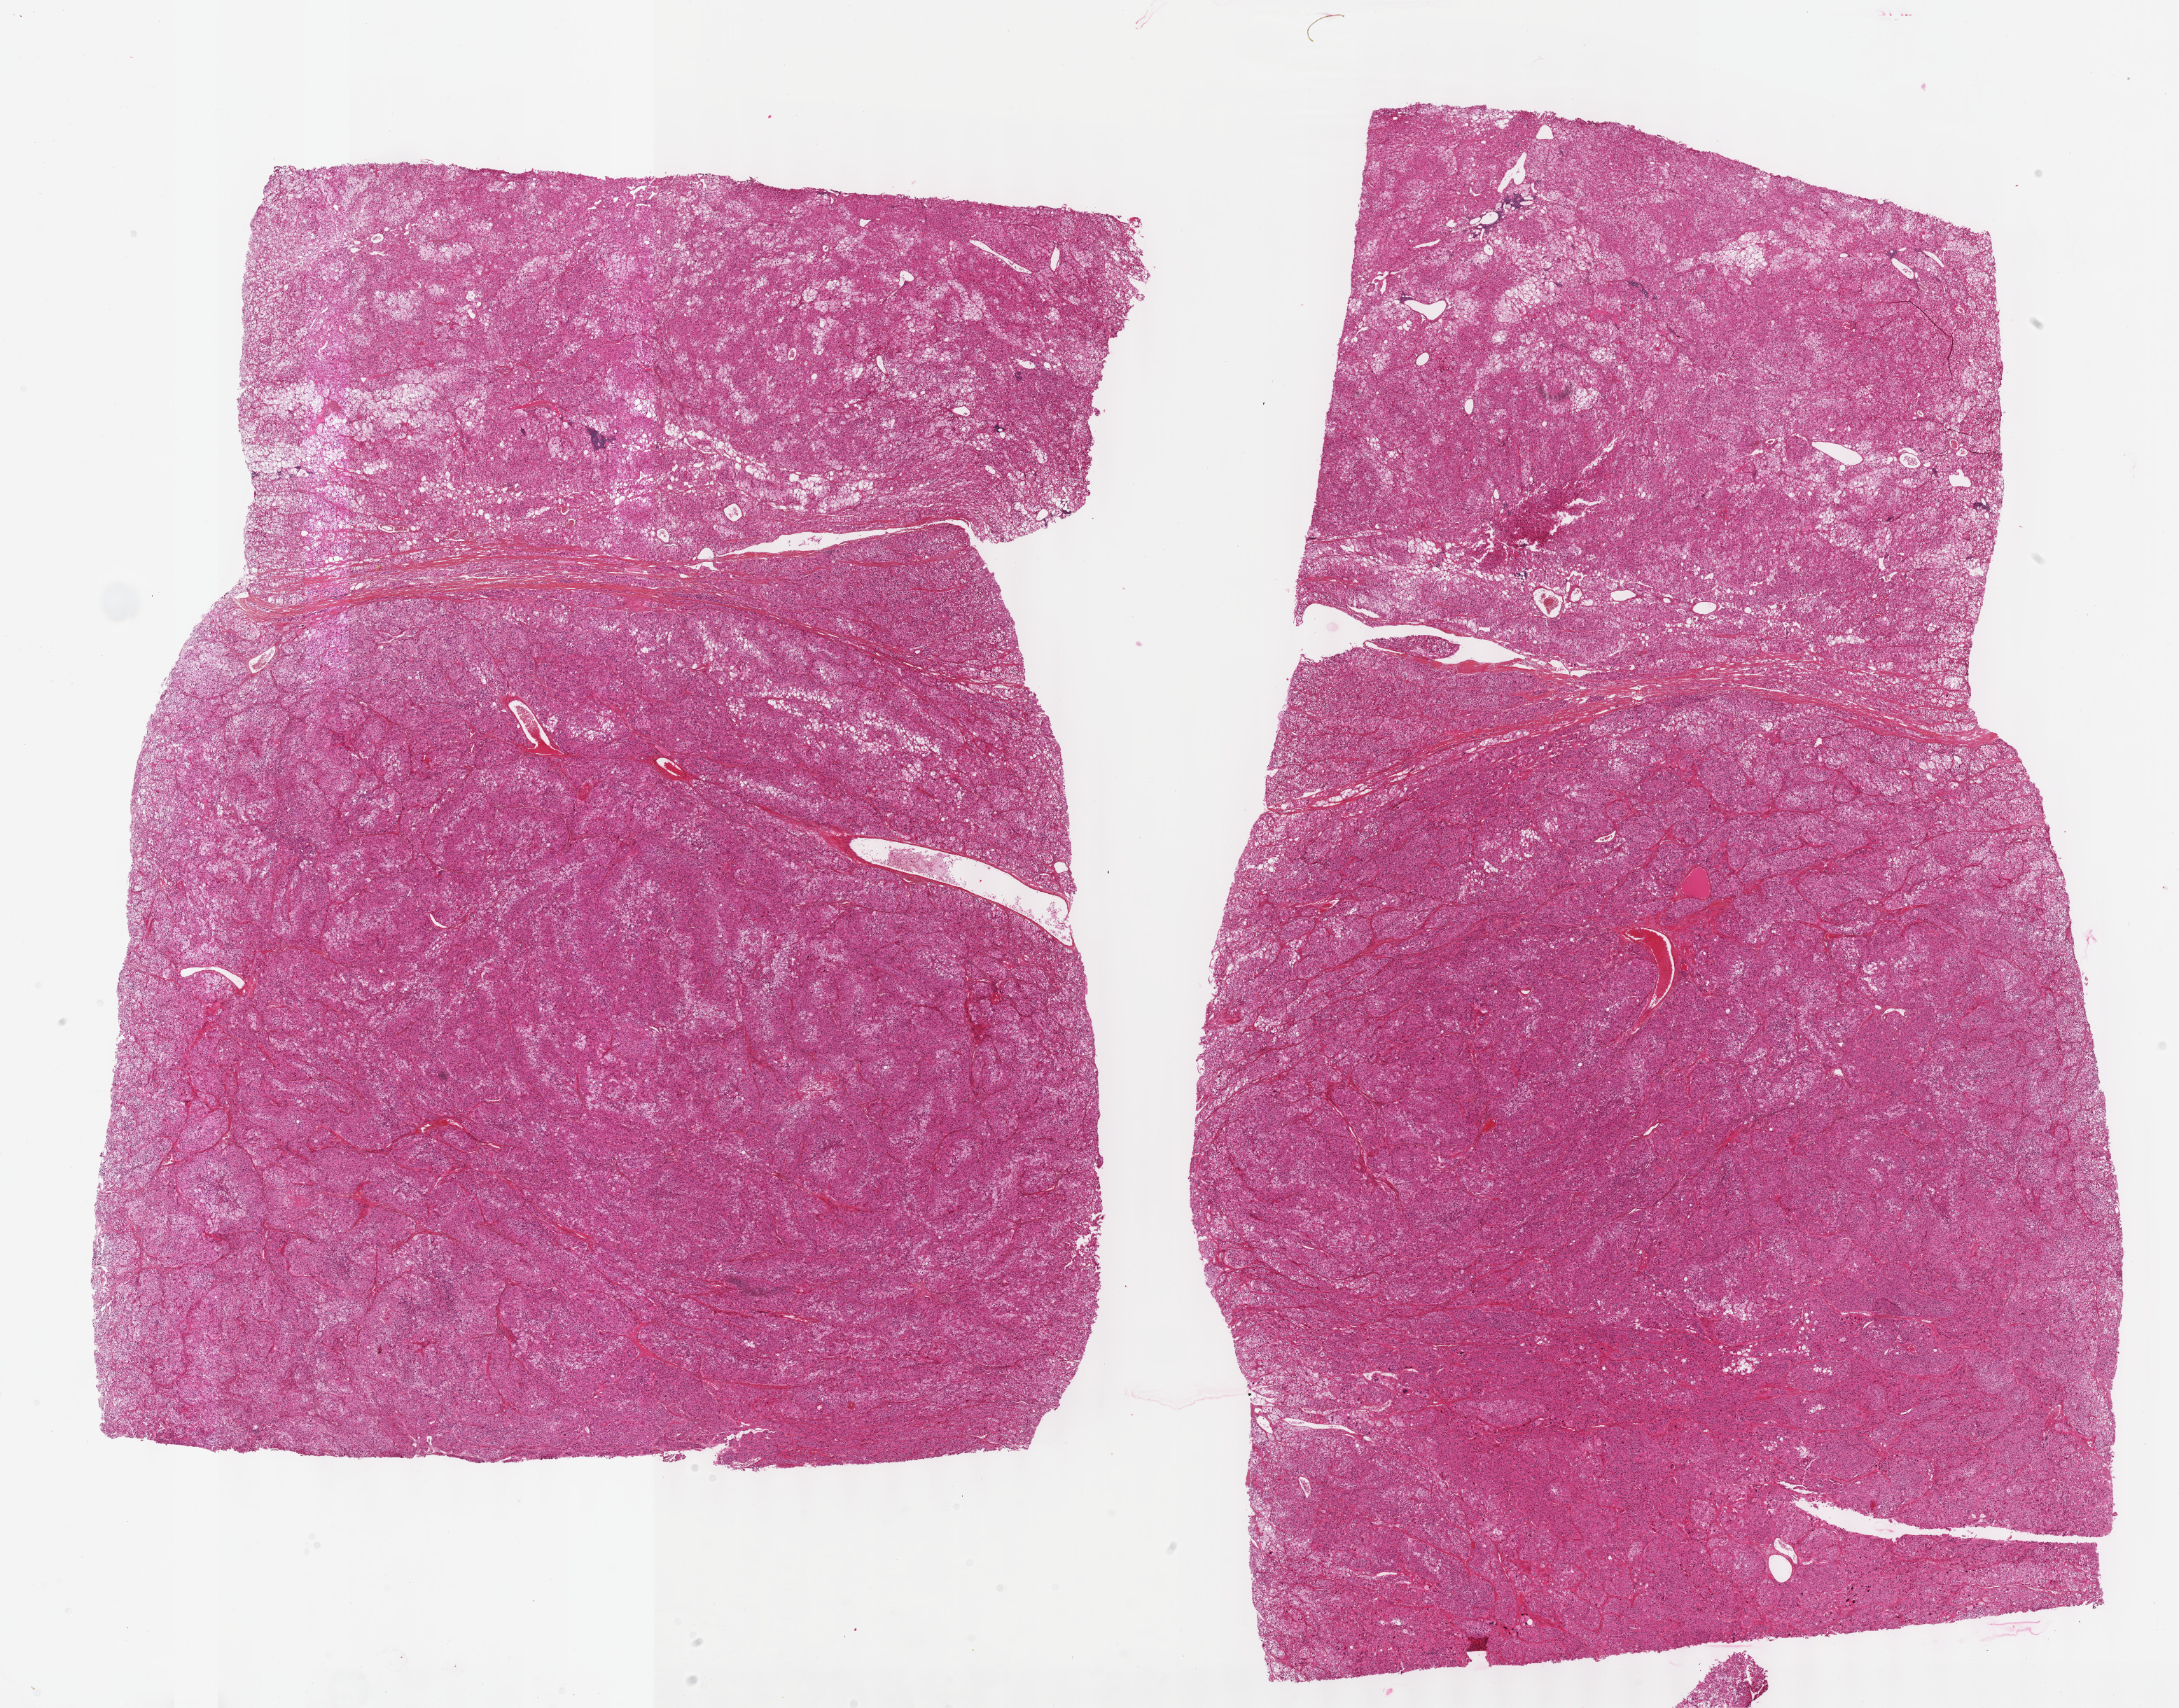
Hematoxylin and eosin (H&E) stained whole-slide image, whole scanned area (about 25.1 x 19.7 mm) shown as a low-resolution overview; formalin-fixed paraffin-embedded (FFPE) diagnostic section; primary tumour sample from the adrenal cortex. Female, age 75 years at initial diagnosis.
Lymph nodes positive (case pathology): 0 of 10 examined. Histologic diagnosis: Adrenal cortical carcinoma (cortex of adrenal gland).